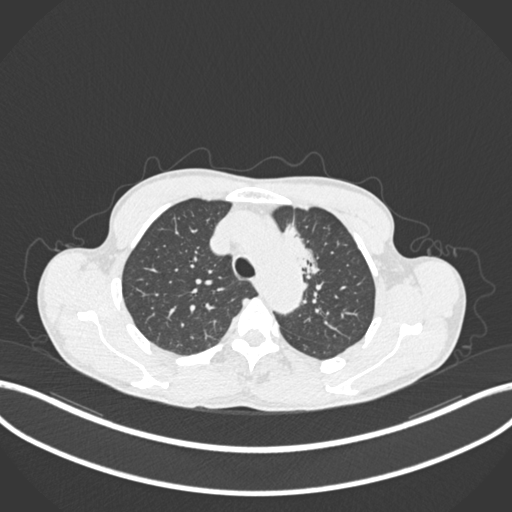
Chest CT, one axial slice. Slice 154 of 211 in the series (ordered by position). 120 kVp. Lung window (W 1500 / L -600 HU). 1 mm slice thickness. 512 × 512 image matrix, field of view 400 × 400 mm. Patient: male, 58 years. Case-level facts recorded for this patient, not image findings: clinical TNM (as recorded): T1c N1 M0.
Annotated regions visible in this slice (bounding box drawn by a radiologist):
- lung tumour (recorded histology: adenocarcinoma): bounding box (x1, y1, x2, y2) in pixels: (283, 219, 321, 283)